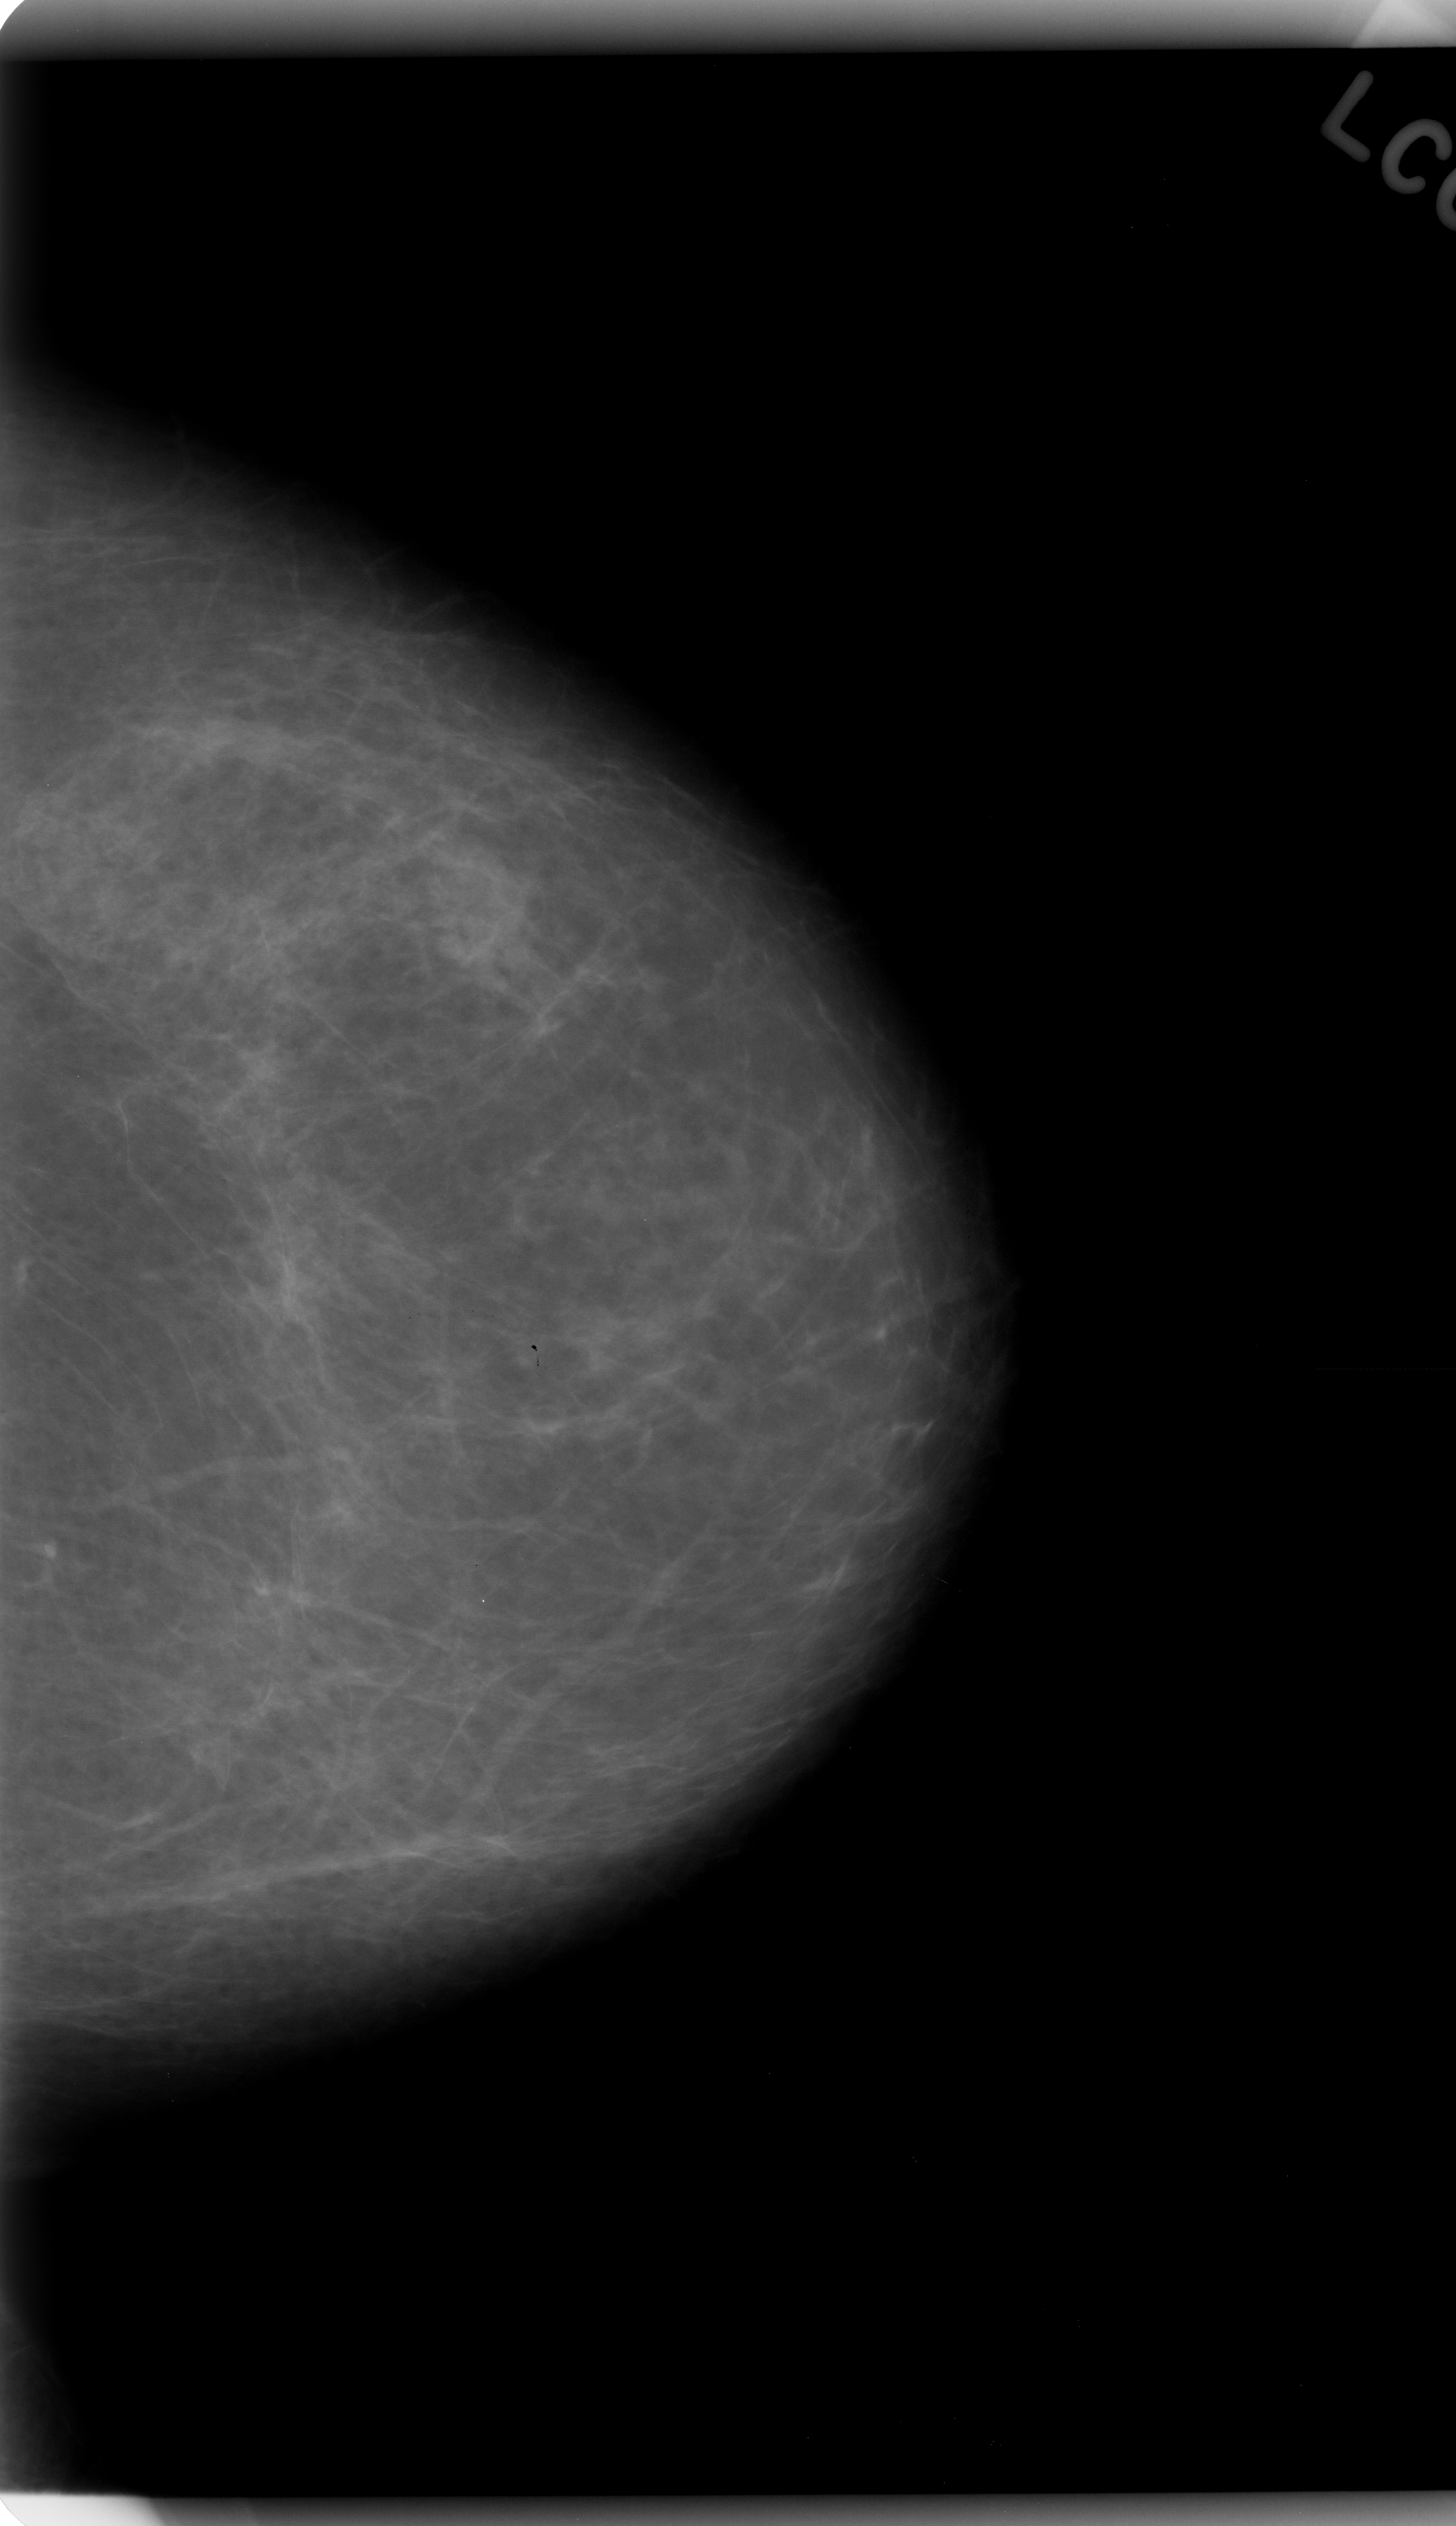
Digitized screen-film mammogram, left breast, CC view, breast composition: almost entirely fatty (BI-RADS density category 1 of 4).
Radiologist-marked abnormalities on this image: mass, shape oval, margins microlobulated; BI-RADS assessment category 4; subtlety rating 4 on a 1 (subtle) to 5 (obvious) scale; pathology (as recorded): malignant.